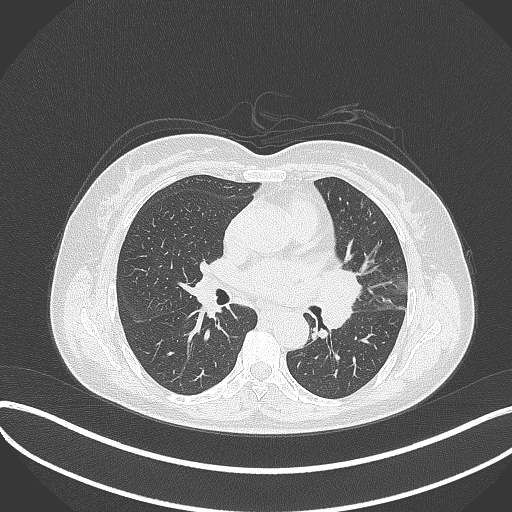
Chest CT, one axial slice. Position 187 of 373 along the scan axis. Reconstruction kernel B70f. 120 kVp. Lung window (W 1500 / L -600 HU). 1 mm slice thickness. 512 × 512 image matrix. Female patient, age 54 years. Case-level facts recorded for this patient, not image findings: clinical TNM (as recorded): T2a N1 M0.
Outlined on this slice (bounding box drawn by a radiologist):
- lung tumour (recorded histology: small cell carcinoma): bounding box <319,264,366,332> (left, top, right, bottom; pixels)